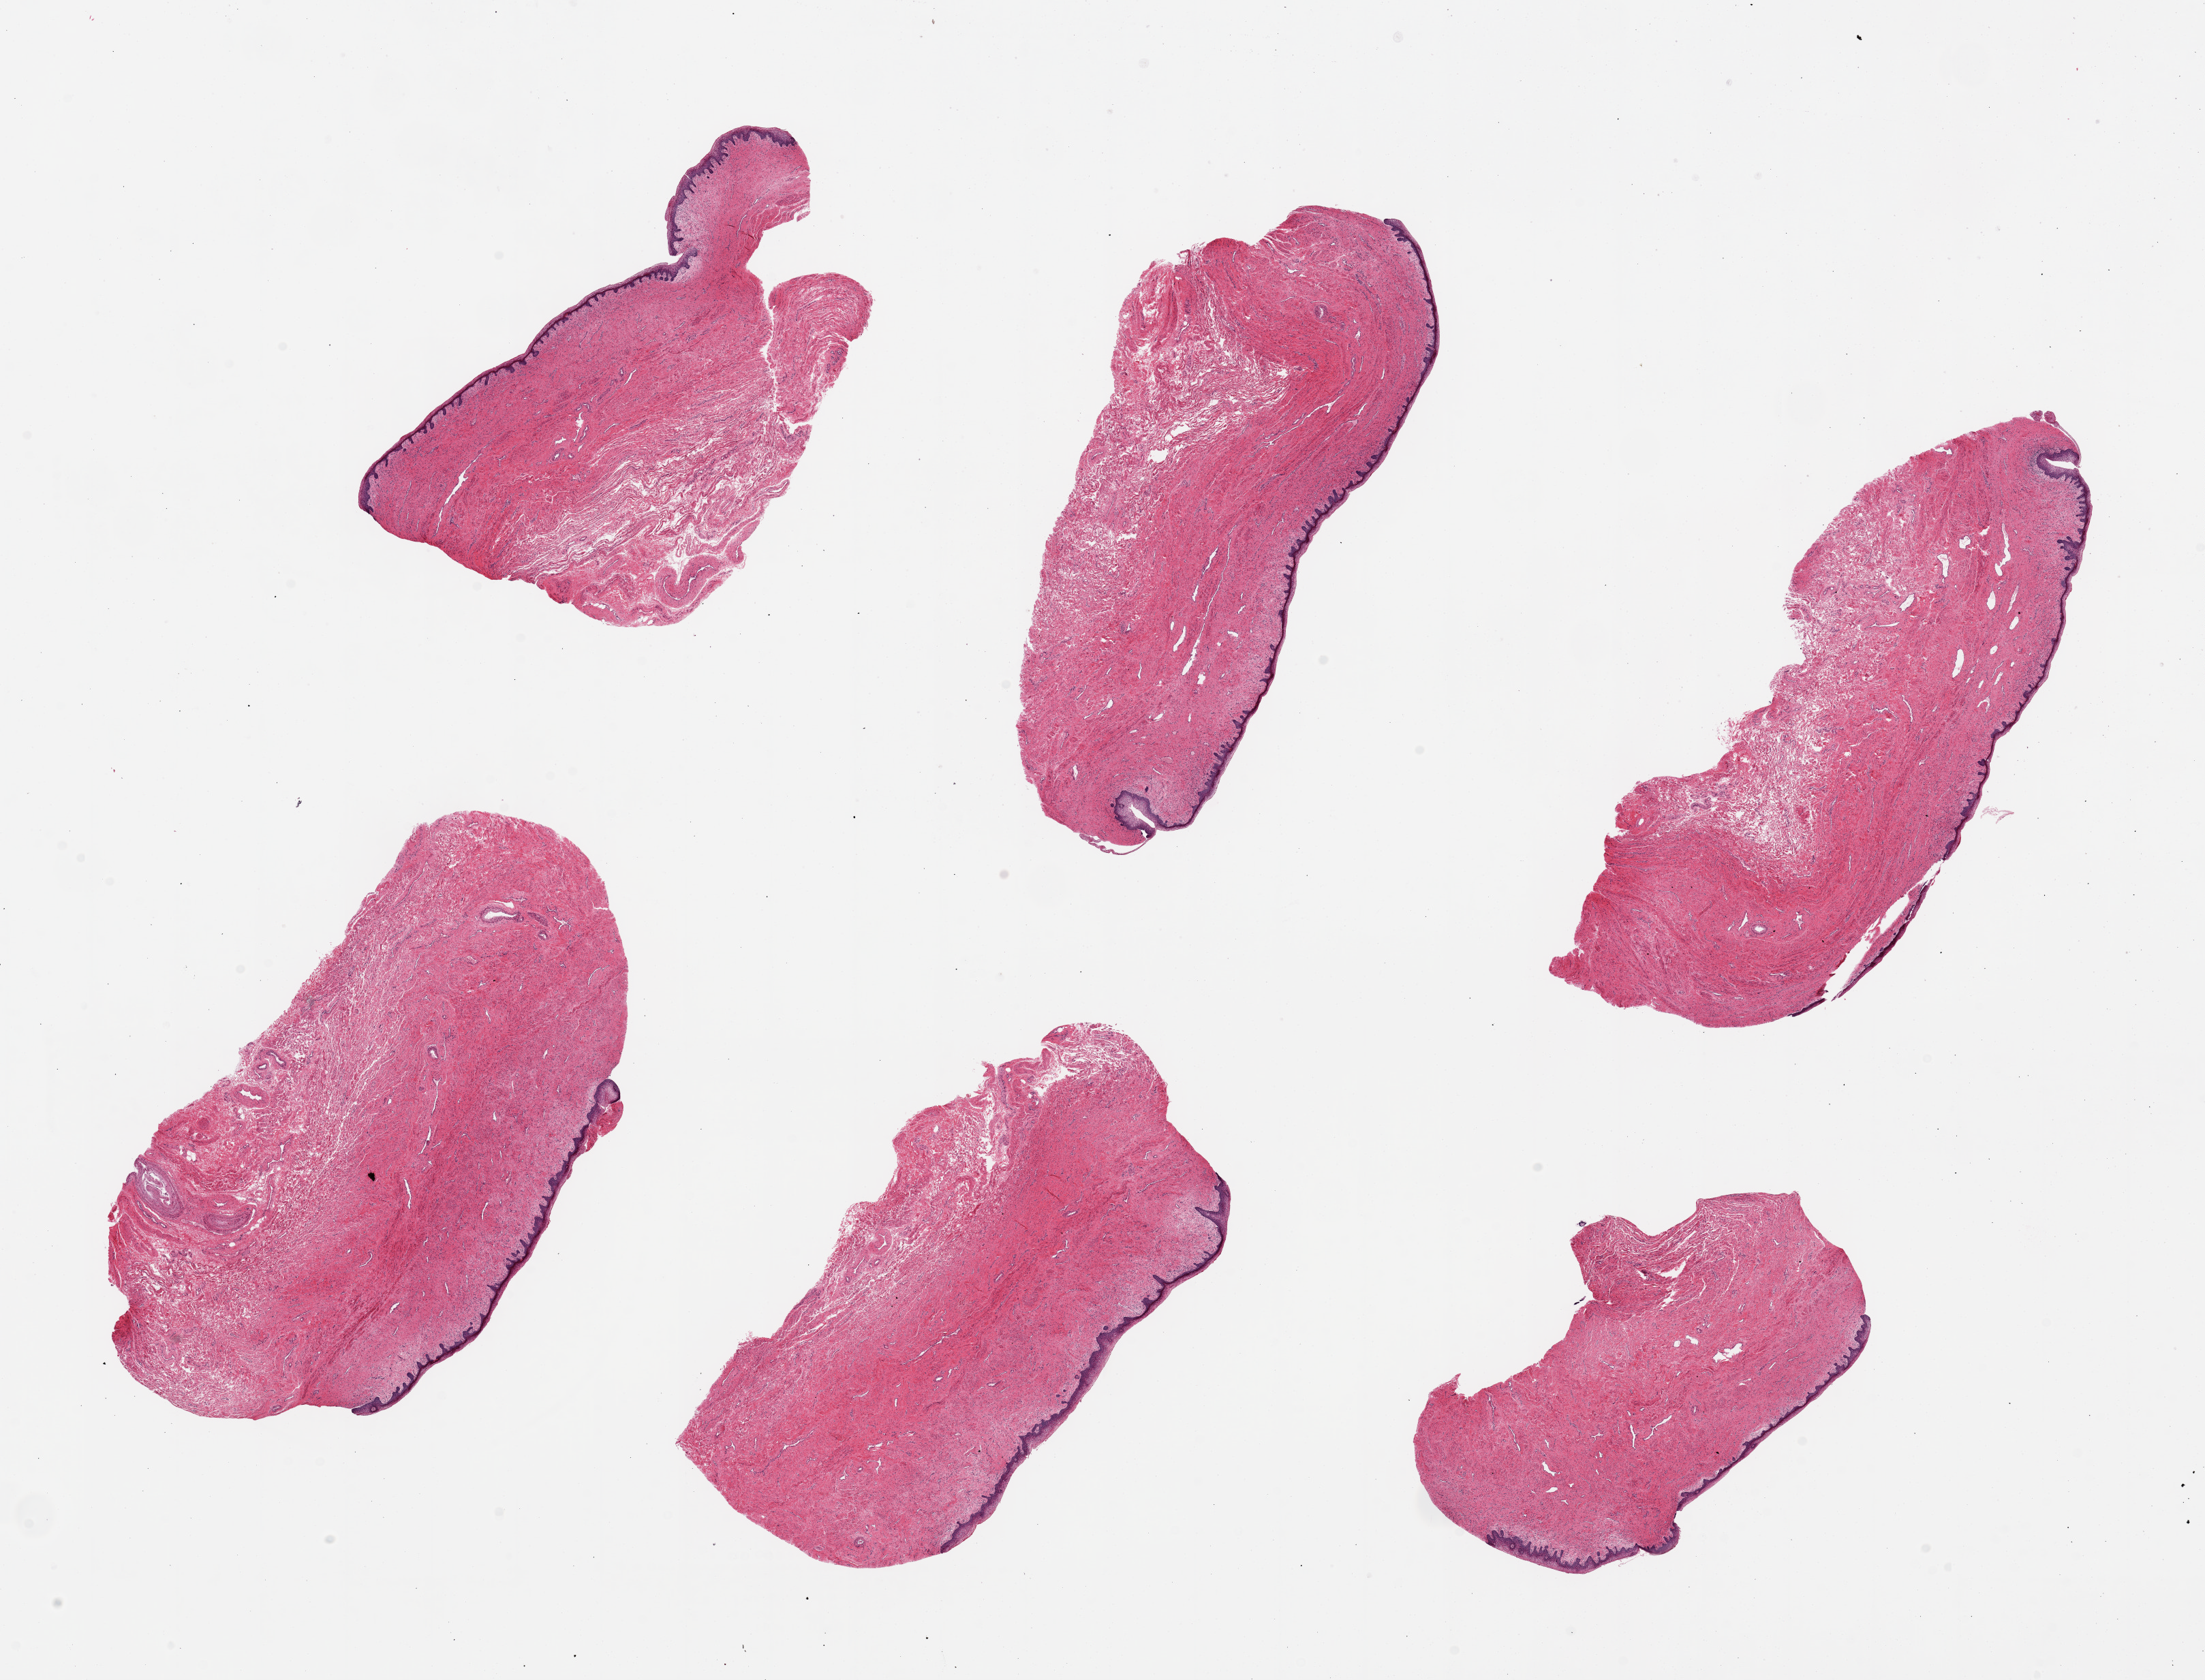
H&E whole-slide image, brightfield — a low-resolution overview of the entire scanned area, about 25.6 x 19.5 mm. PAXgene-fixed, paraffin-embedded tissue. Sampled site (target tissue): vagina. Tissue donor sample. Donor: female.
Pathologist's review note for this sample: 6 pieces, up to 8x4mm.